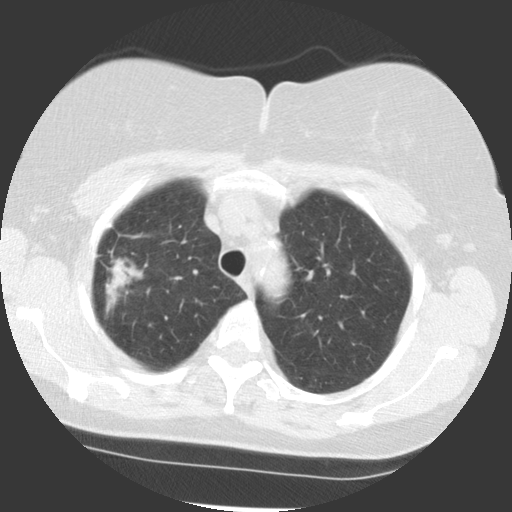
Chest CT (low-dose screening protocol), one axial image; first (baseline) screen; lung window (W 1500 / L -600 HU); 2.5 mm slice thickness; standard (soft-tissue) reconstruction kernel (STANDARD). Female participant, aged 68 years at enrolment. Former smoker at enrolment.
Expert-annotated lung lesion, bounding box (x1, y1, x2, y2) in pixels: (91, 250, 146, 307). Reader record for this screening exam (exam-level; its link to the box is not recorded): non-calcified nodule or mass ≥4 mm, right upper lobe, 42 × 20 mm, spiculated (stellate) margins, soft tissue attenuation. Official screen result: positive, change unspecified: nodule(s) >= 4 mm or enlarging nodule(s), mass(es), or other non-specific abnormalities suspicious for lung cancer. Participant outcome: lung cancer diagnosed 51 days after this screen — adenocarcinoma, NOS, right upper lobe, moderately differentiated (G2), stage IB (AJCC 6th edition), 31 mm at pathology.